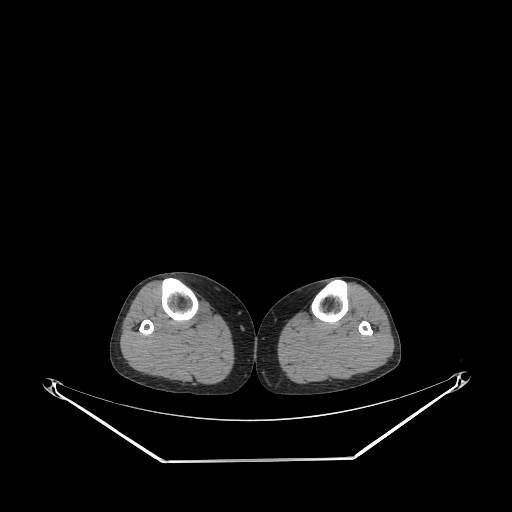
CT of an extremity soft-tissue mass (from a PET/CT study), one axial slice; position 153 of 267 along the scan axis; reconstruction kernel STANDARD; soft-tissue window (W 400 / L 40 HU); 3.75 mm slice thickness; 512 × 512 image matrix. Female patient. From the clinical record (not read from this slice): histological type: undifferentiated – high grade; grade: high; site of the primary tumour: right thigh.
Outlined on this slice (expert contour drawn on MRI and transferred to this co-registered scan by the dataset authors):
- gross tumour volume (mass): box from (x=196, y=301) to (x=213, y=325) px